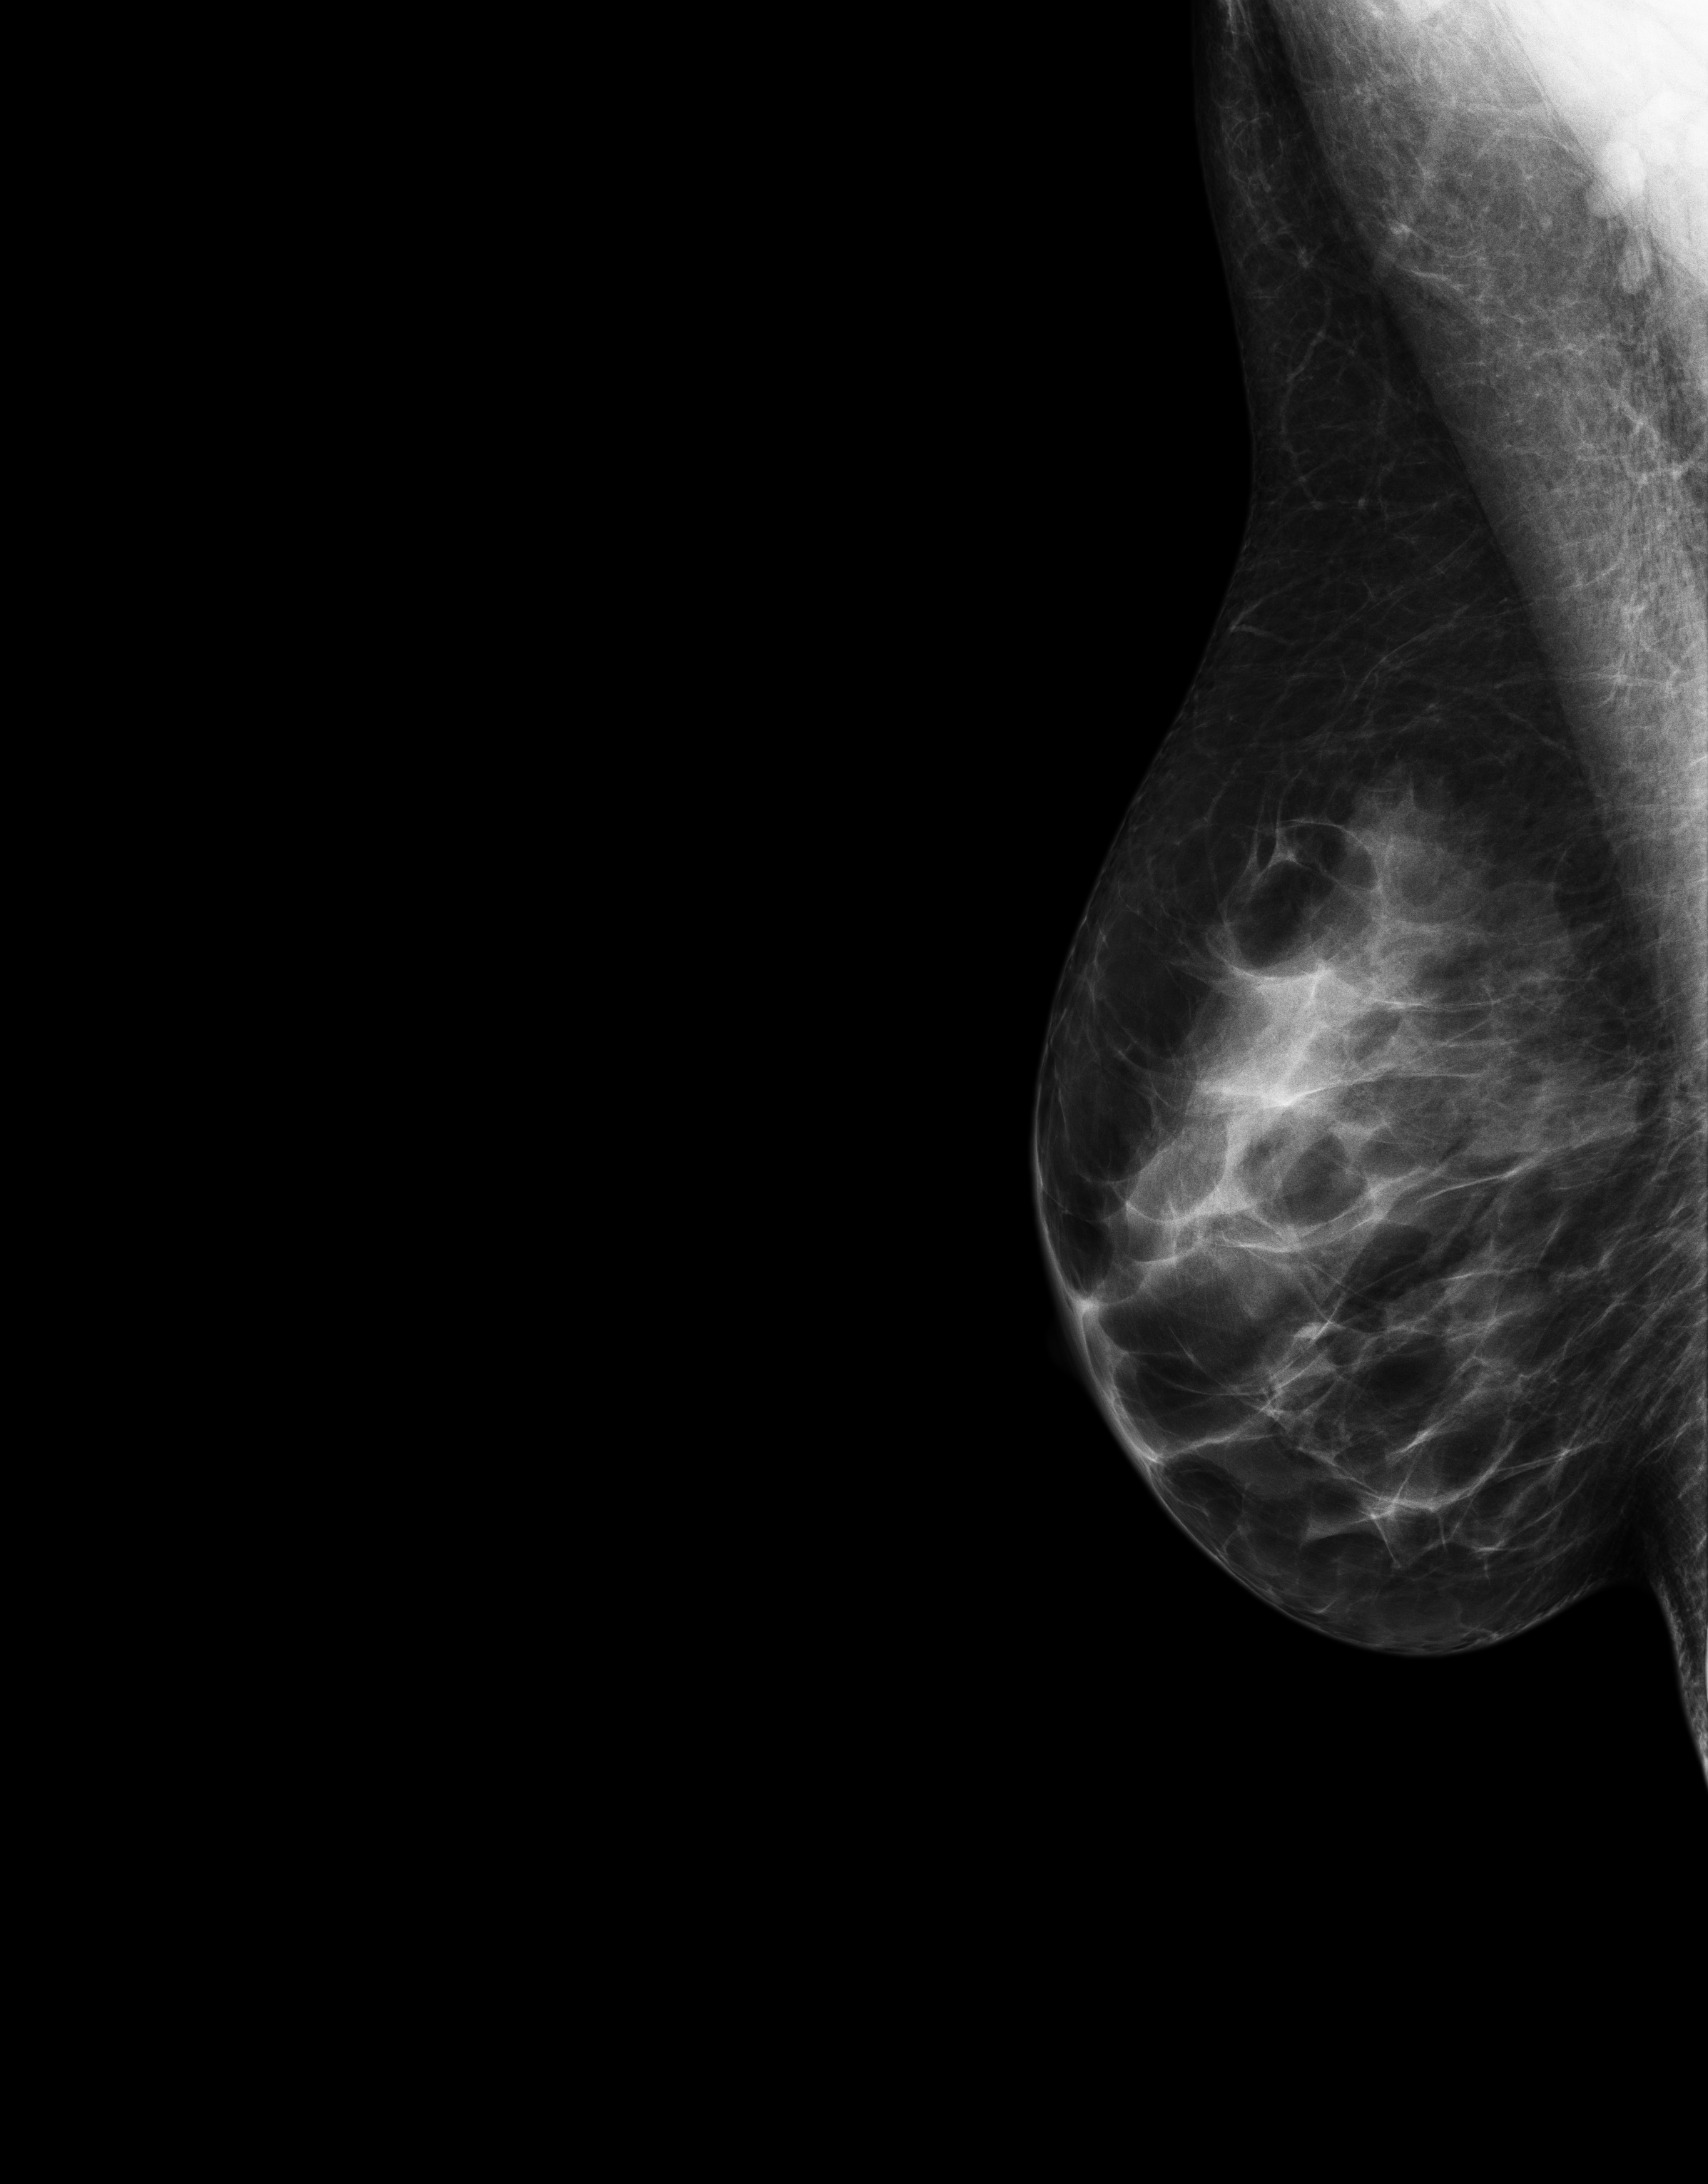
Full-field digital mammogram (FFDM); right breast; medio-lateral oblique projection; annual screening mammography examination. Patient: female, 51 years.
BI-RADS breast density category at the screening exam (both breasts, scale 1–4): 3. Final BI-RADS assessment for this screening round (tomosynthesis exam, both breasts): category 1. Recall: no recall after this screen.